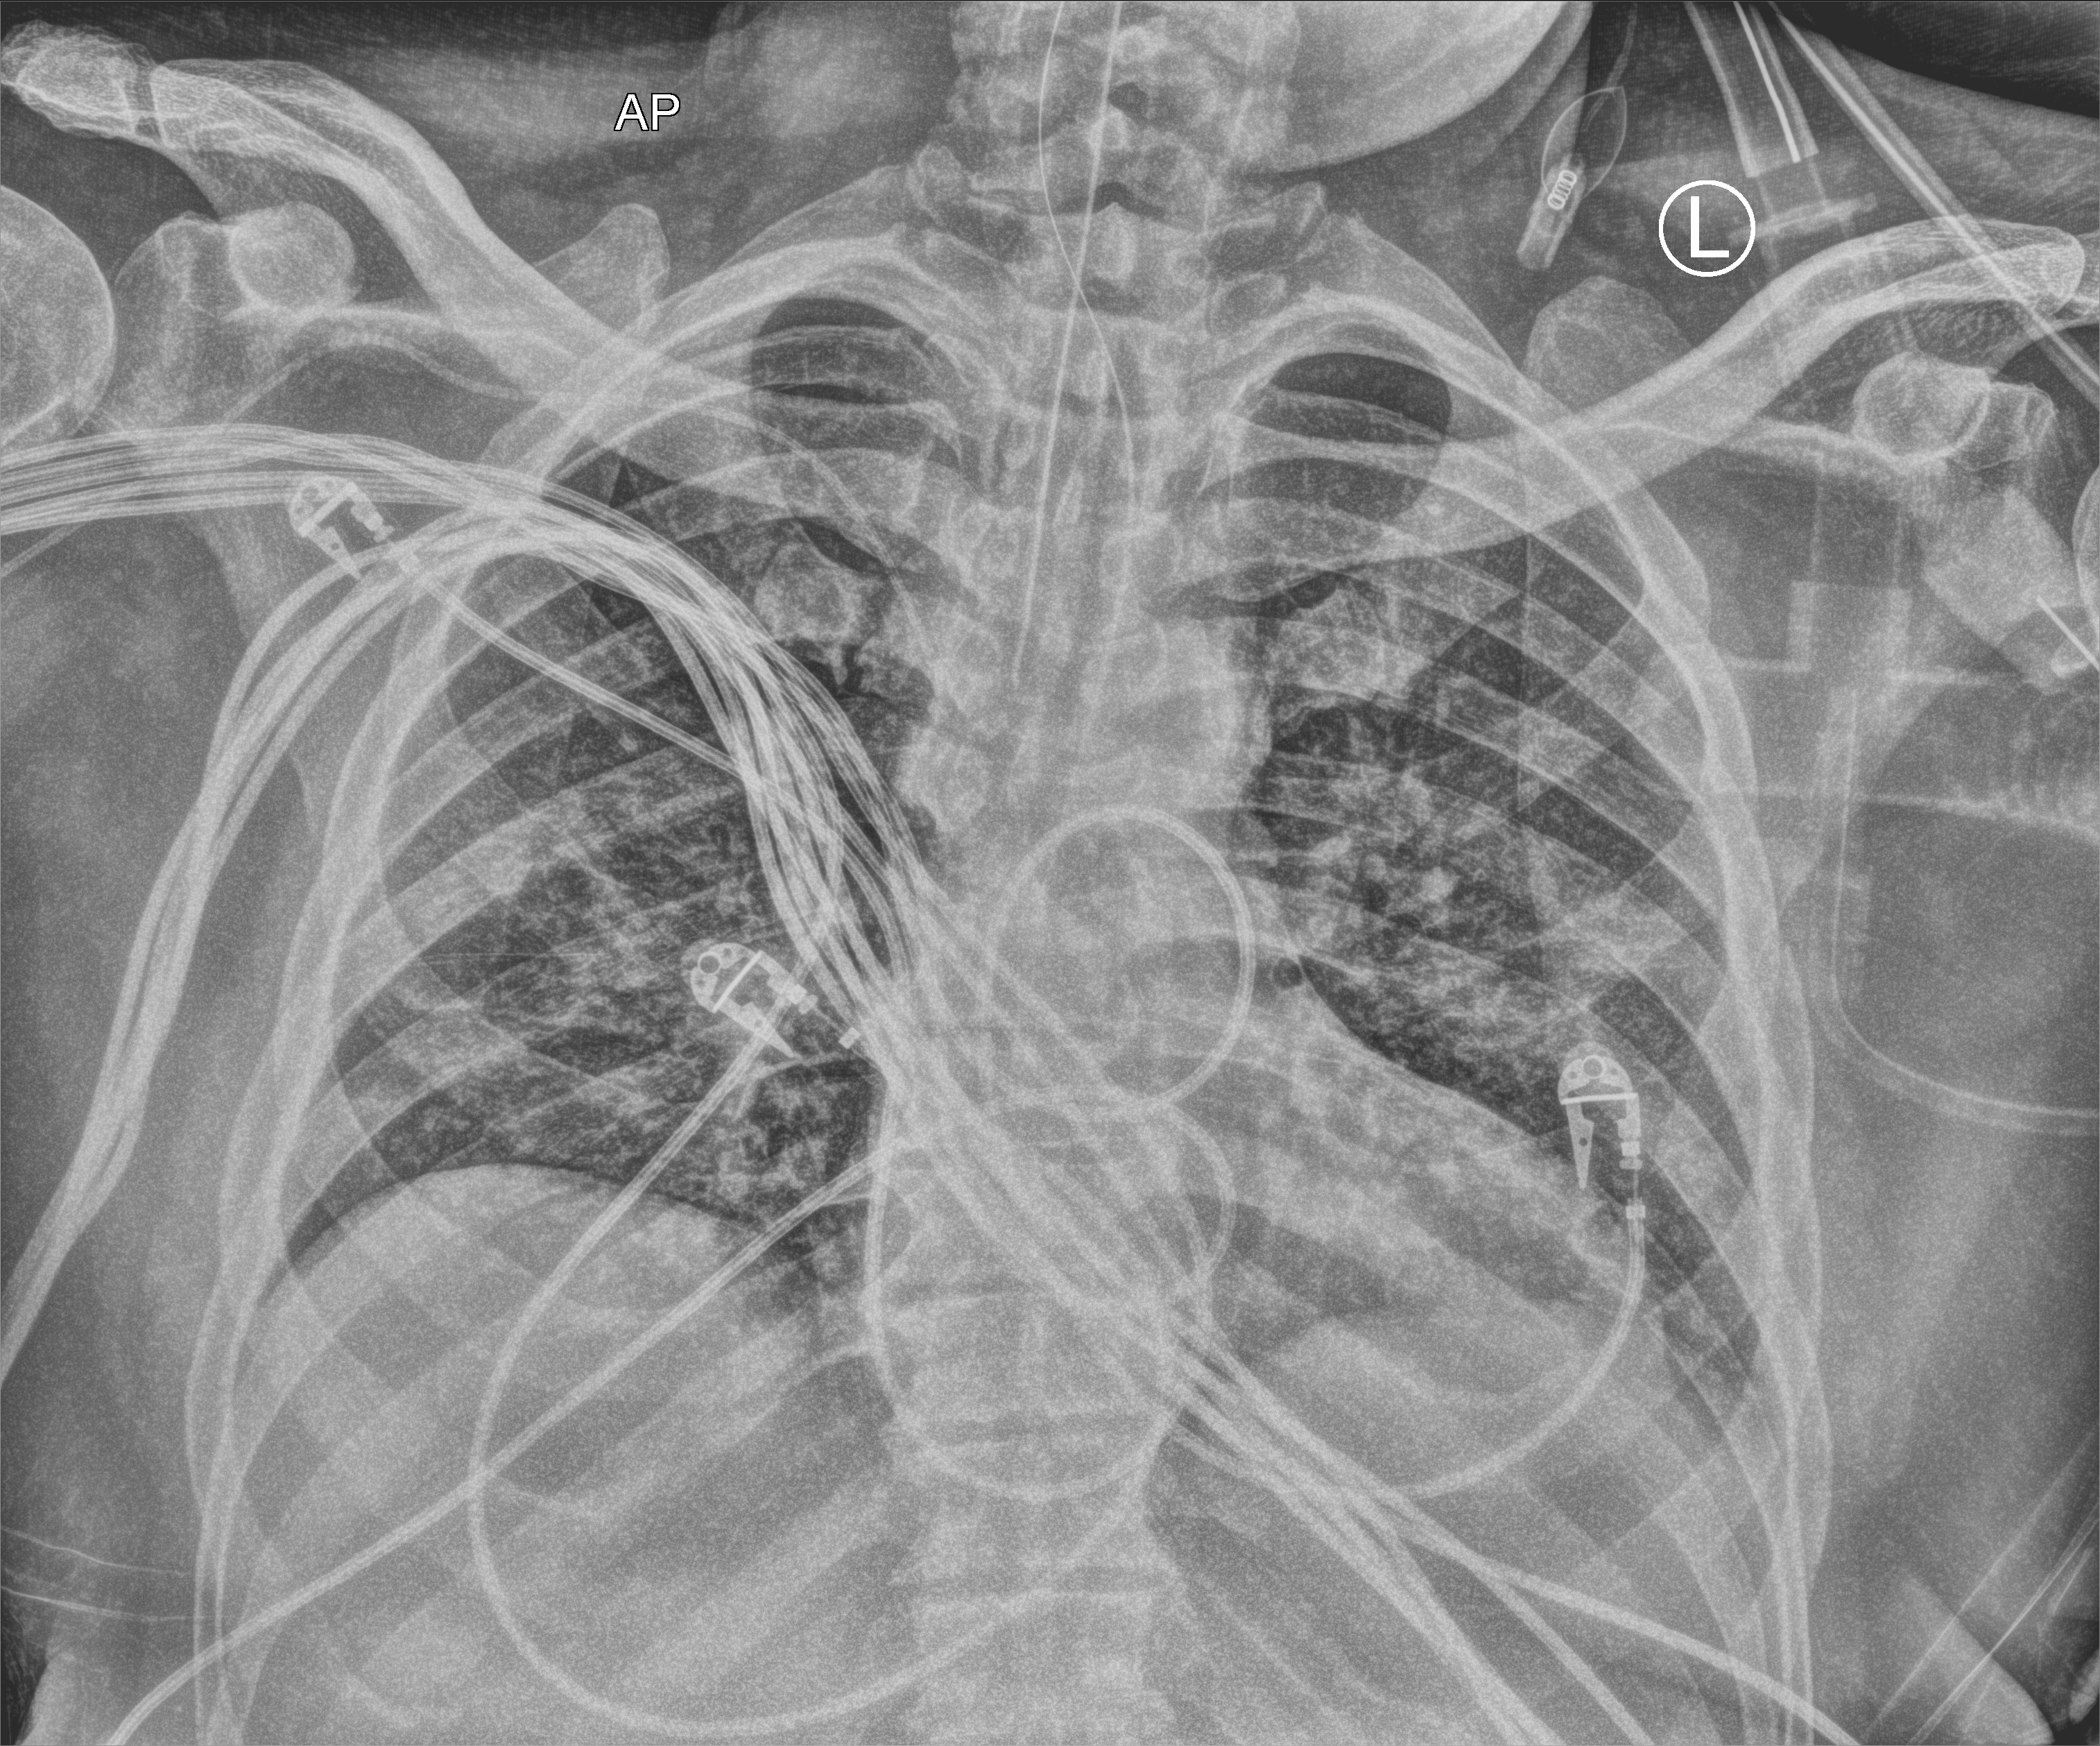
Bedside chest radiograph (computed radiography). Male patient hospitalised with COVID-19, age 18–59 years.
From the hospital-stay record, not from the radiograph (when in the stay this image was taken is not recorded):
- length of hospital stay: 41 days
- mechanically ventilated during this hospital stay: yes
- COPD (admission record): no